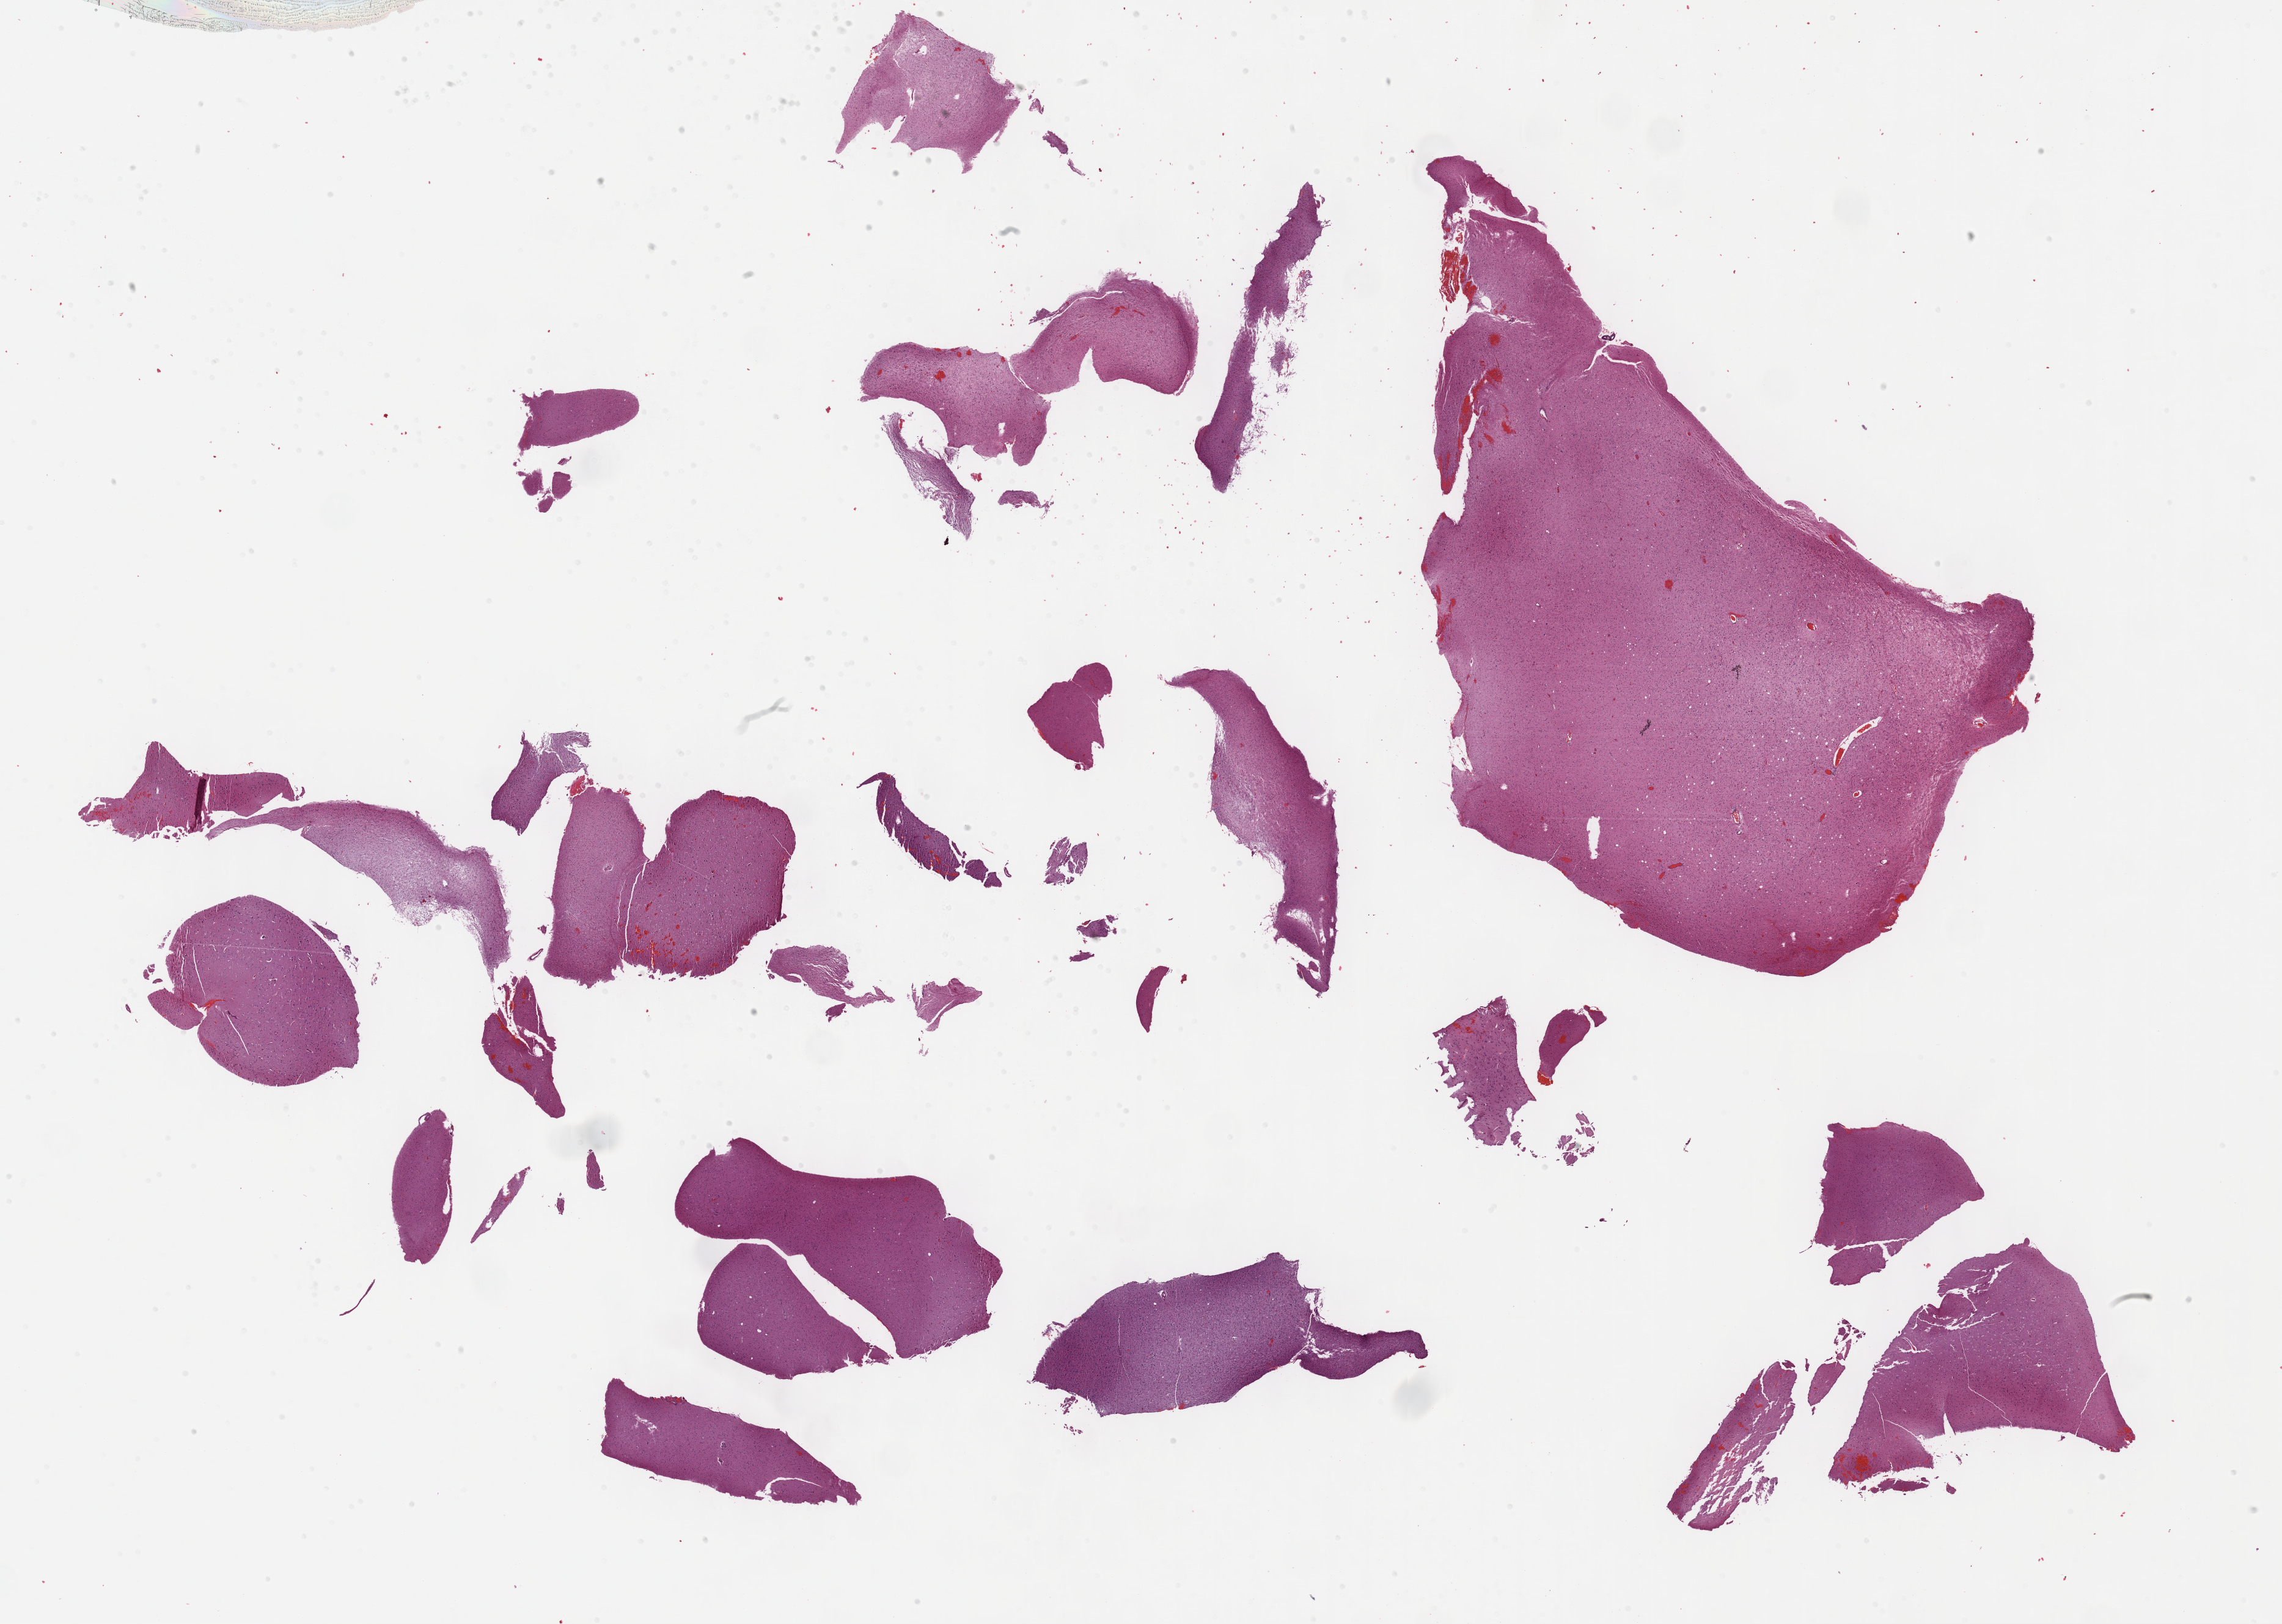
H&E whole-slide image — low-resolution overview of the scanned area, about 30.2 x 21.5 mm (from a 40x scan); formalin-fixed paraffin-embedded (FFPE) diagnostic section; brain, primary tumour sample. Female patient; age at initial diagnosis 18 years. Histologic grade: G2 (moderately differentiated).
Laterality: left. Pathologic diagnosis: Mixed glioma.